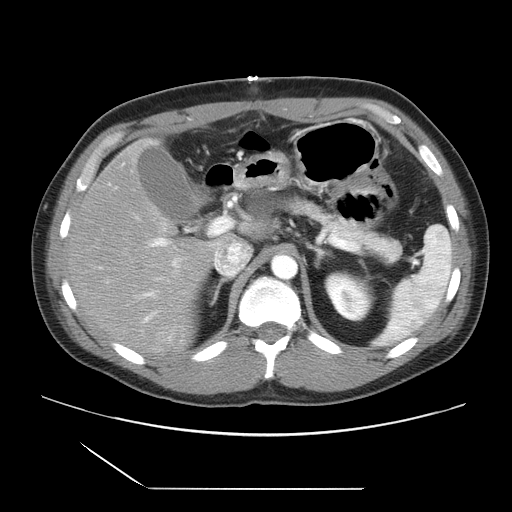
Contrast-enhanced abdominal CT, one axial slice; position 16 of 39 along the scan axis; 120 kVp; soft-tissue window (W 400 / L 40 HU); 512 × 512 image matrix, field of view 395 × 395 mm. Male patient, age 39 years. Case-level facts recorded for this patient, not image findings: diagnosis: colorectal cancer liver metastases, imaged before liver resection; multiple liver metastases: yes; largest metastasis: 1.3 cm; disease in both lobes: no.
Annotated regions visible in this slice (manually delineated by an expert):
- hepatic veins: box from (x=212, y=242) to (x=249, y=275) px
- liver: (x=69, y=142)–(x=230, y=356)
- planned liver remnant (the part of the liver to remain after resection): (x=124, y=143)–(x=145, y=166)
- portal vein (with intrahepatic branches): (x=99, y=183)–(x=232, y=333)